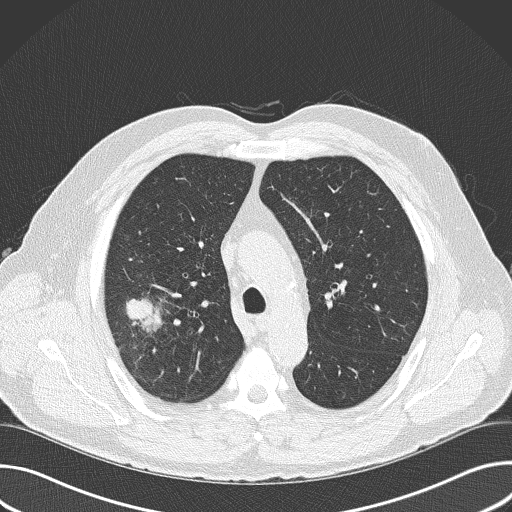
Axial slice from a low-dose chest CT screening exam, first (baseline) screen, lung window (W 1500 / L -600 HU), 2 mm slice thickness, 120 kVp, 512 × 512 image matrix. Male participant, aged 56 years at enrolment. Current smoker at enrolment.
• Expert-annotated lung lesion, box from (x=83, y=269) to (x=191, y=382) px.
• Reader record for this screening exam (exam-level; its link to the box is not recorded): non-calcified nodule or mass ≥4 mm, right upper lobe, 6 × 5 mm, spiculated (stellate) margins, soft tissue attenuation.
• Official screen result: positive, change unspecified: nodule(s) >= 4 mm or enlarging nodule(s), mass(es), or other non-specific abnormalities suspicious for lung cancer.
• Lung cancer was diagnosed 16 days after this screen: adenocarcinoma, NOS, right upper lobe, poorly differentiated (G3), stage IIB (AJCC 6th edition), 60 mm at pathology.